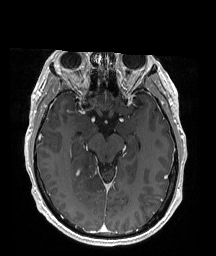
Brain MRI from a brain-tumour surgery series, one axial slice; position 111 of 176 along the scan axis; T1-weighted post-contrast; 216 × 256 image matrix. From the clinical record (not read from this slice): histopathology: Oligodendroglioma; WHO grade: 2; IDH mutation: yes.
Structures marked on this image (manually delineated by an expert):
- tumour: bounding box (x1, y1, x2, y2) in pixels: (70, 150, 99, 205)